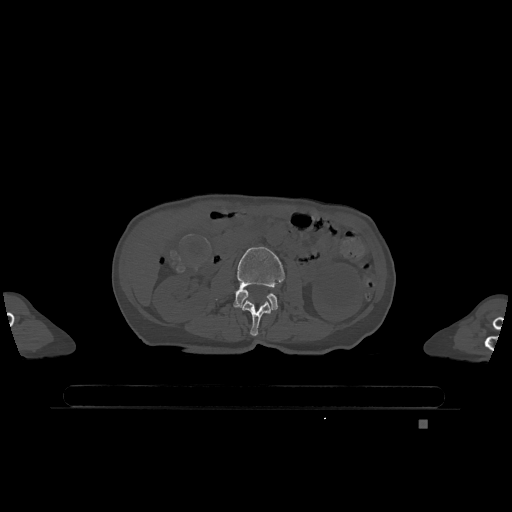
CT including the spine, one axial slice; position 382 of 1317 along the scan axis; bone window (W 1800 / L 400 HU); 512 × 512 image matrix. Female patient, age 74 years. Case-level facts recorded for this patient, not image findings: primary cancer: lung.
Annotated regions visible in this slice (semi-automatic segmentation, software-assisted and operator-edited):
- L2 vertebra: box from (x=242, y=300) to (x=271, y=336) px
- L3 vertebra: (x=233, y=247)–(x=285, y=310)